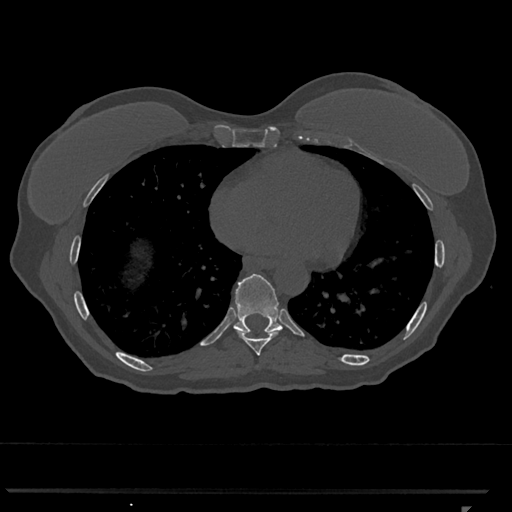
CT including the spine, one axial slice. Slice 643 of 793 in the series (ordered by position). Reconstruction kernel Br40s/3. Bone window (W 1800 / L 400 HU). 512 × 512 image matrix, field of view 380 × 380 mm. Female patient, age 62 years. From the clinical record (not read from this slice): primary cancer: renal.
Outlined on this slice (semi-automatic segmentation, software-assisted and operator-edited):
- T8 vertebra: bounding box [x1, y1, x2, y2] px = [238, 332, 278, 356]
- T9 vertebra: [232, 274, 283, 334]